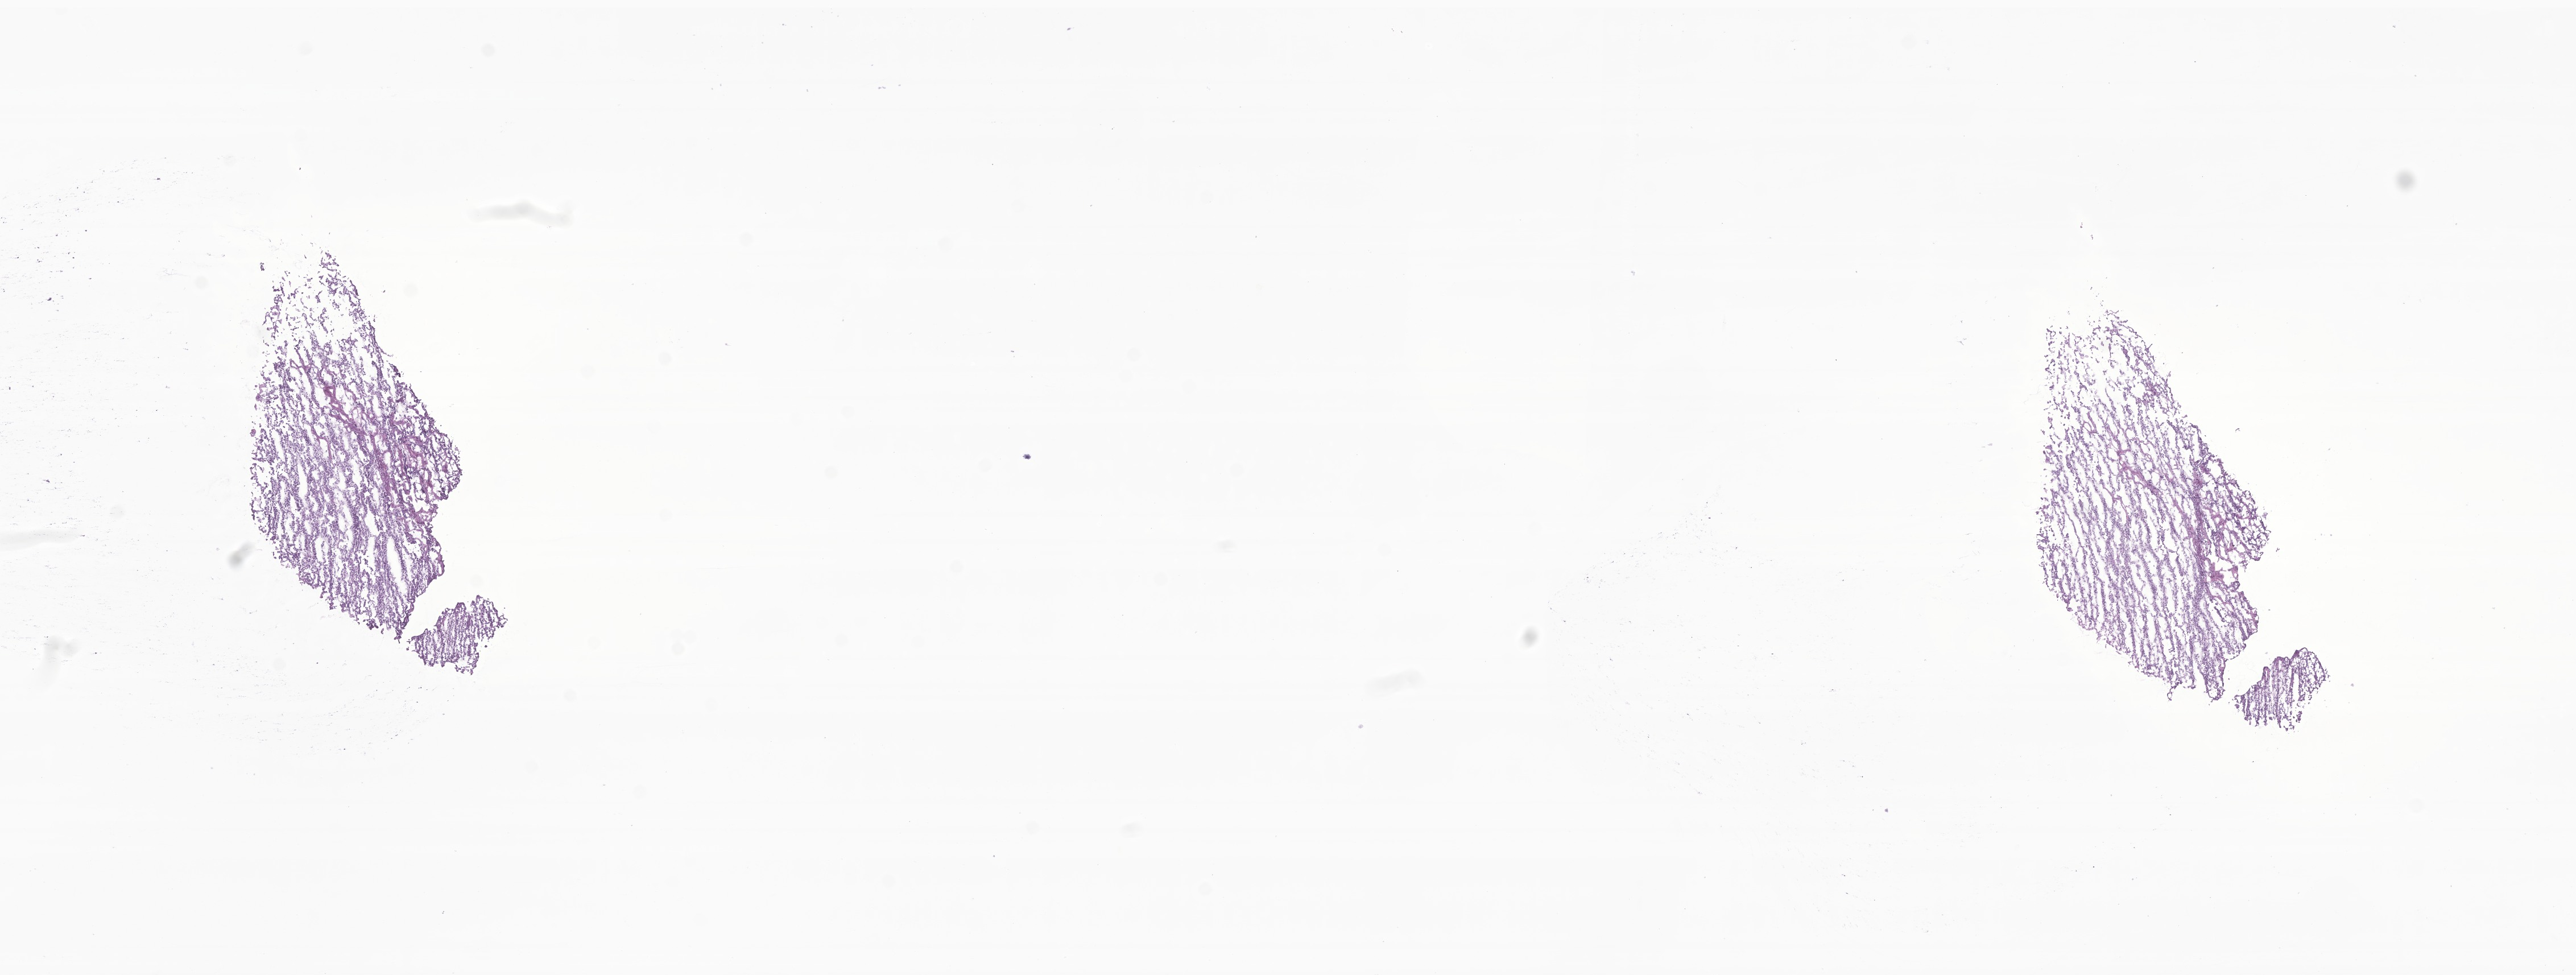
Whole-slide image, H&E stain of tumor tissue from the brain — shown as a low-resolution overview of the whole scanned area (about 19.1 x 7.2 mm), cryosection (OCT / tissue freezing medium). Patient: female, age 112 months.
Diagnosis (ICD-O-3 morphology term): Medulloblastoma, NOS.